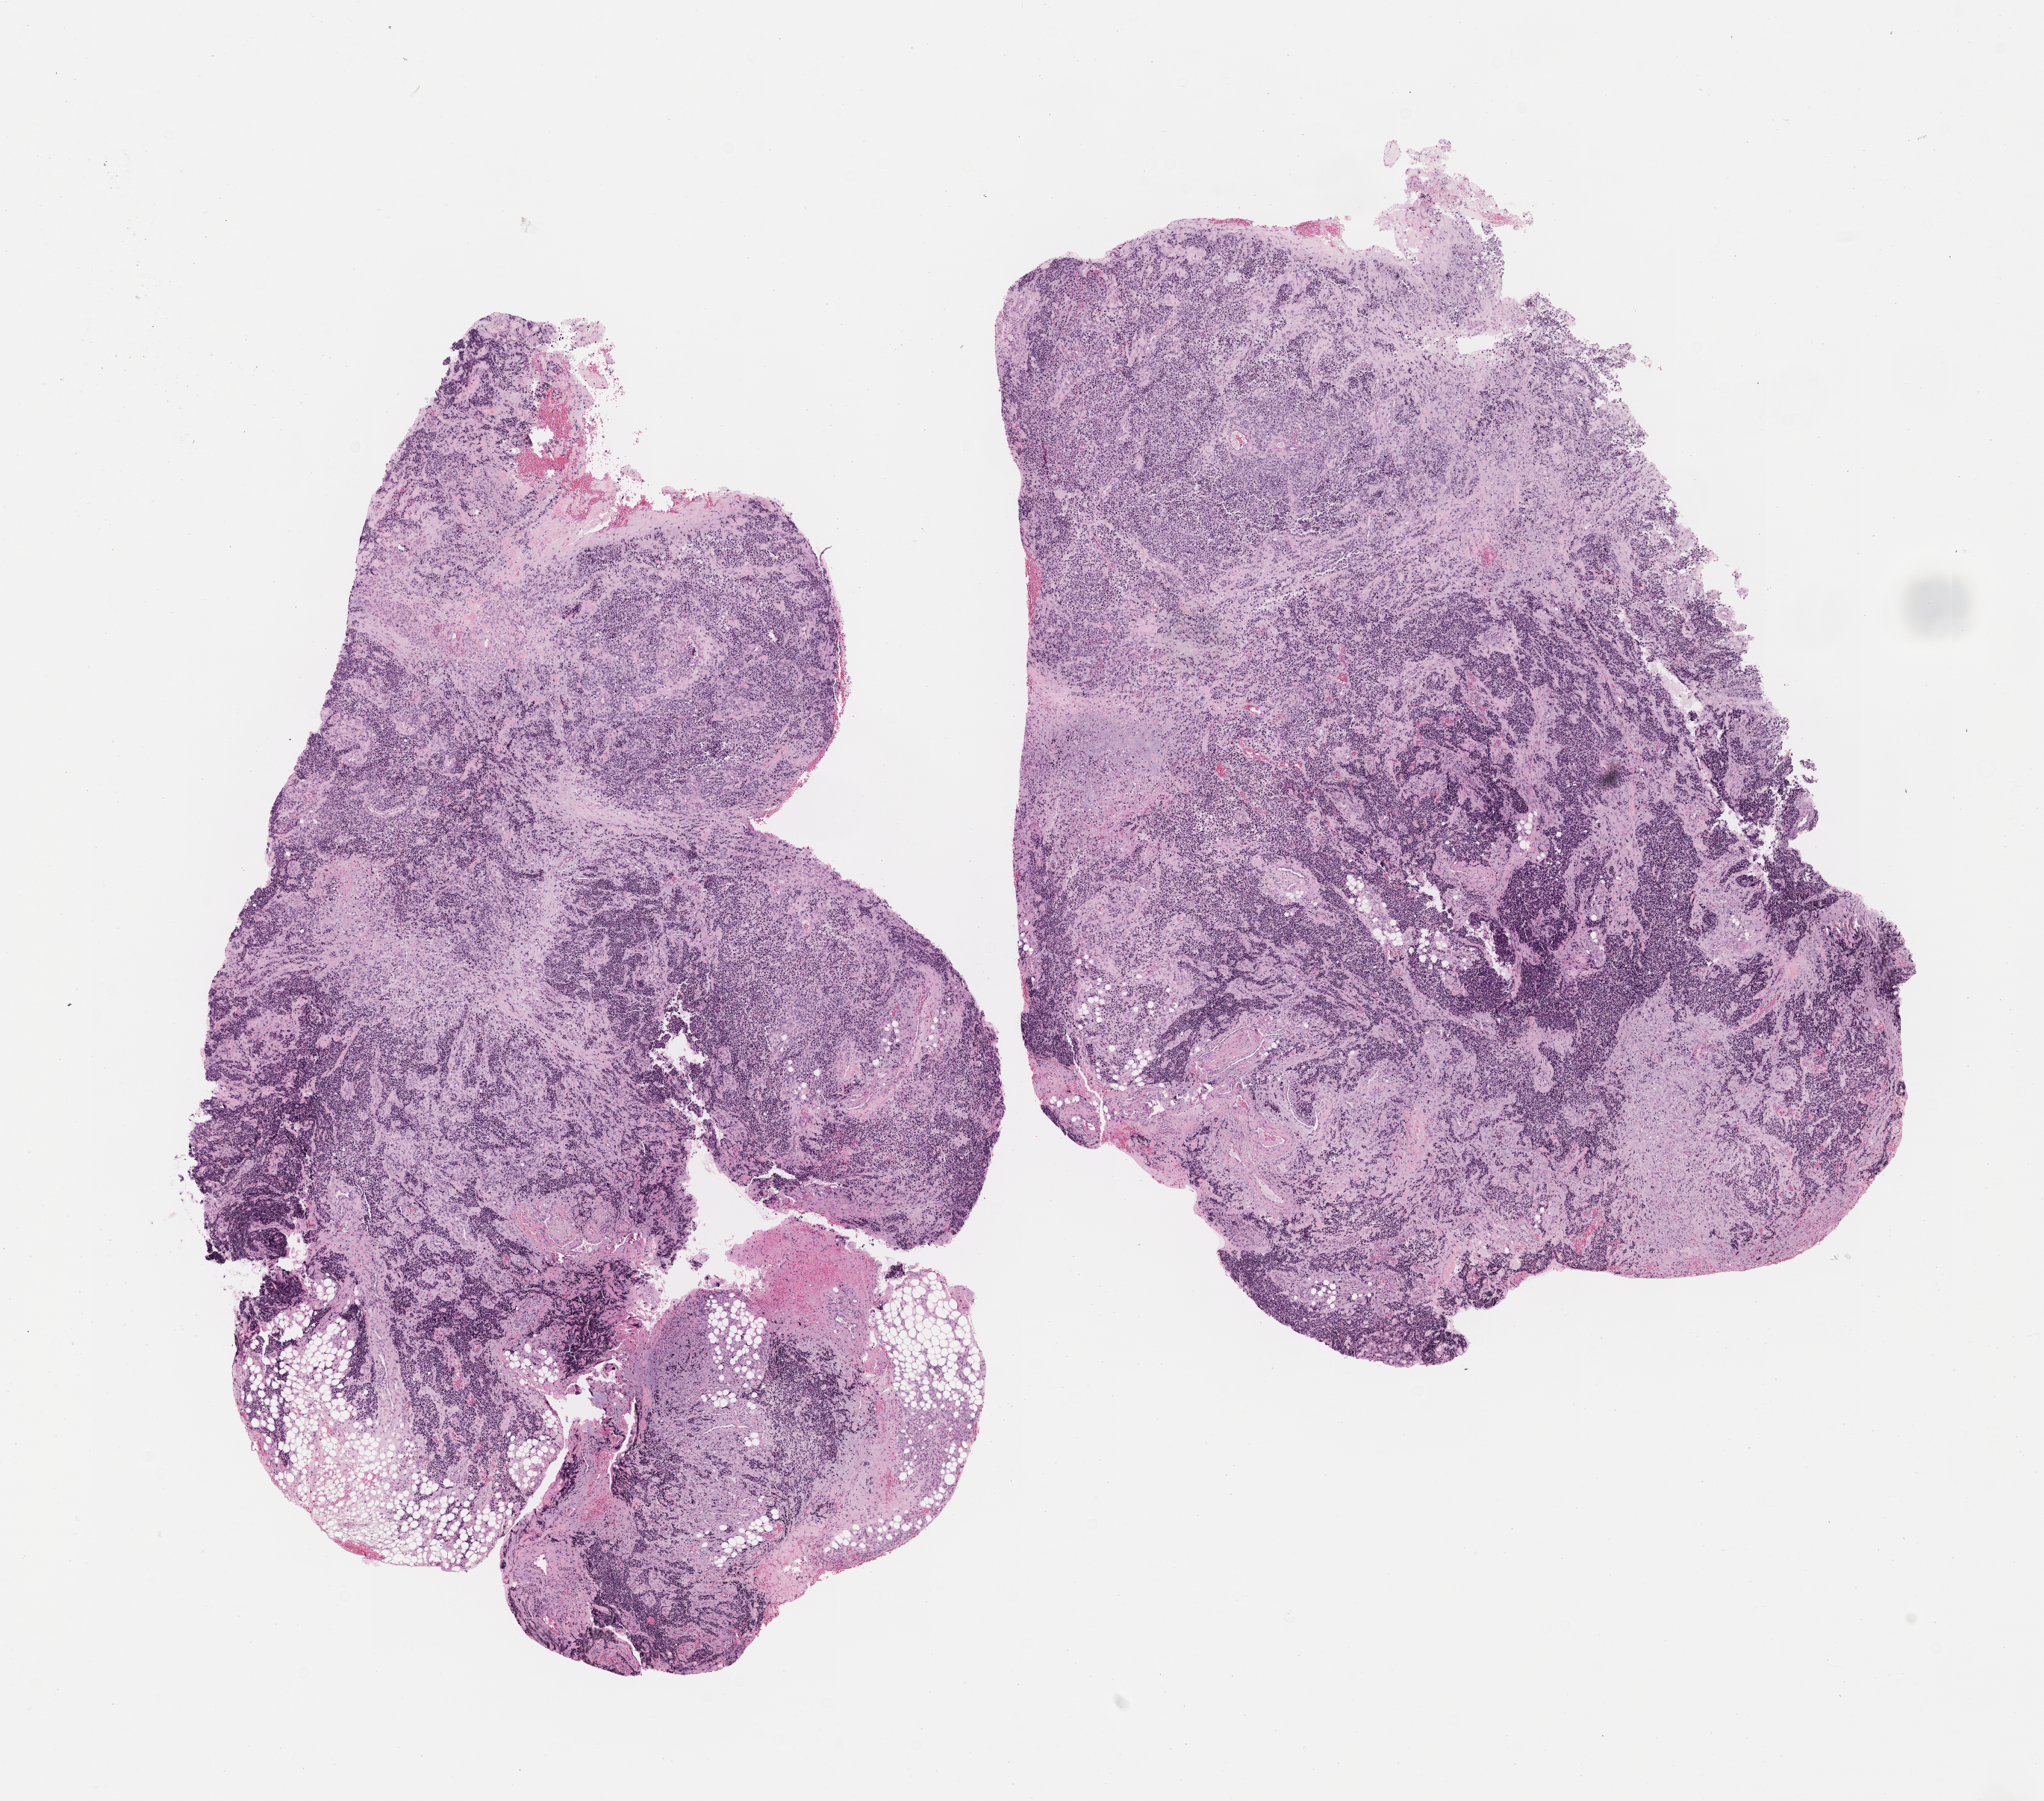
Digitized H&E-stained section of tumor tissue, low-resolution overview of the scanned area, about 11.1 x 9.8 mm; FFPE section; sample anatomic site: soft tissue, forearm. Patient: female, age 9.7 years at diagnosis.
- diagnosis: rhabdomyosarcoma; histological classification: alveolar rhabdomyosarcoma
- stage (as recorded): 4